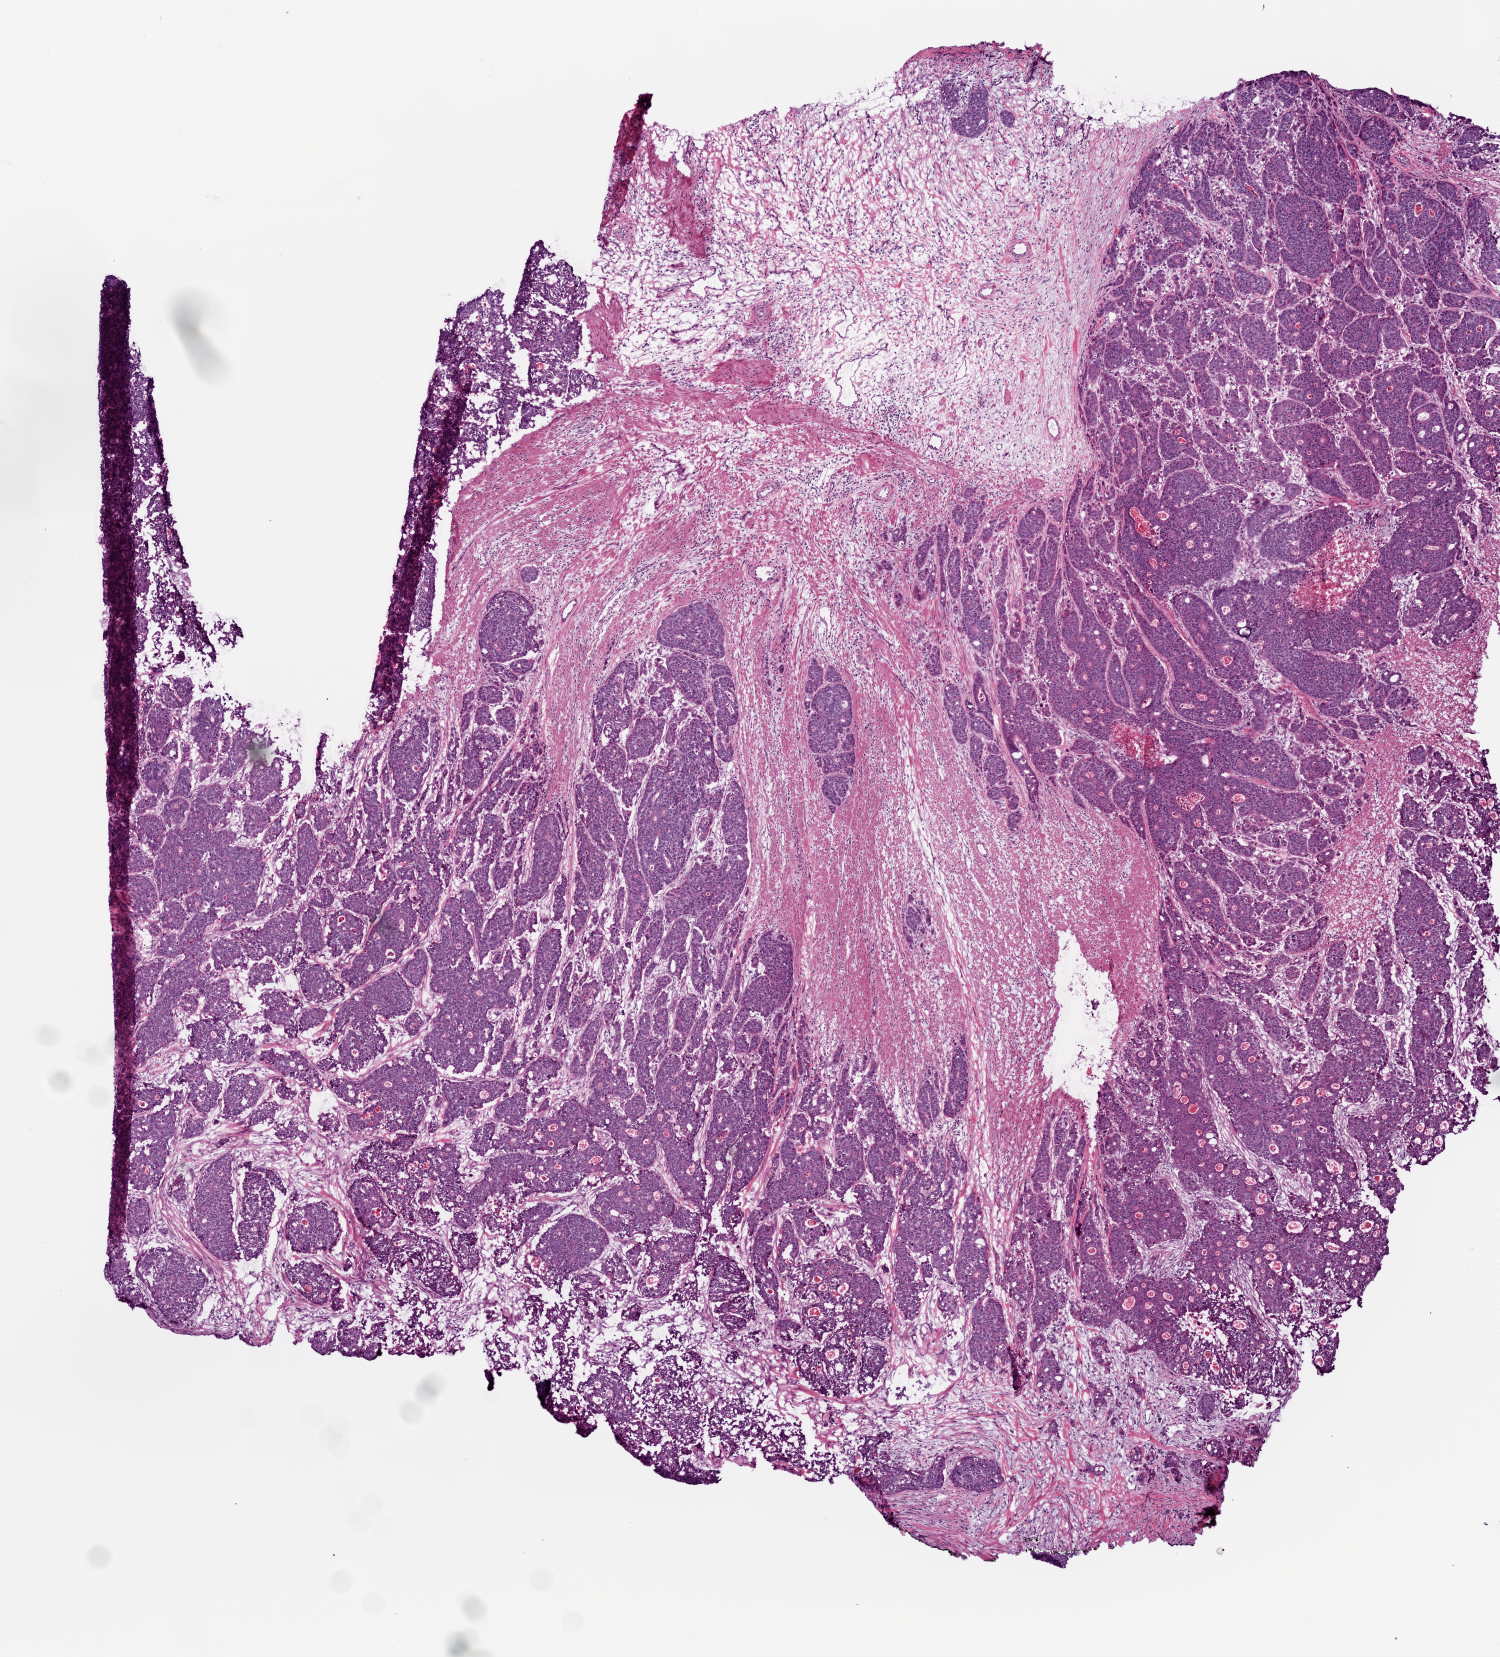
Whole-slide histology image, H&E — a low-resolution overview of the entire scanned area, about 6.0 x 6.6 mm (slide scanned at 20x). Frozen section from the top of the tissue portion. Sample: primary tumour, colon. Male patient; age at initial diagnosis 46 years. Slide review estimates, as recorded: tumour cells 70%, tumour nuclei 80%, normal cells 25%, stromal cells 0%, necrosis 5%. Inflammatory infiltration, as recorded: lymphocyte infiltration 10%, monocyte infiltration 1%, neutrophil infiltration 2%.
AJCC pathologic stage: IVA. Histologic diagnosis: Adenocarcinoma, NOS (splenic flexure of colon).